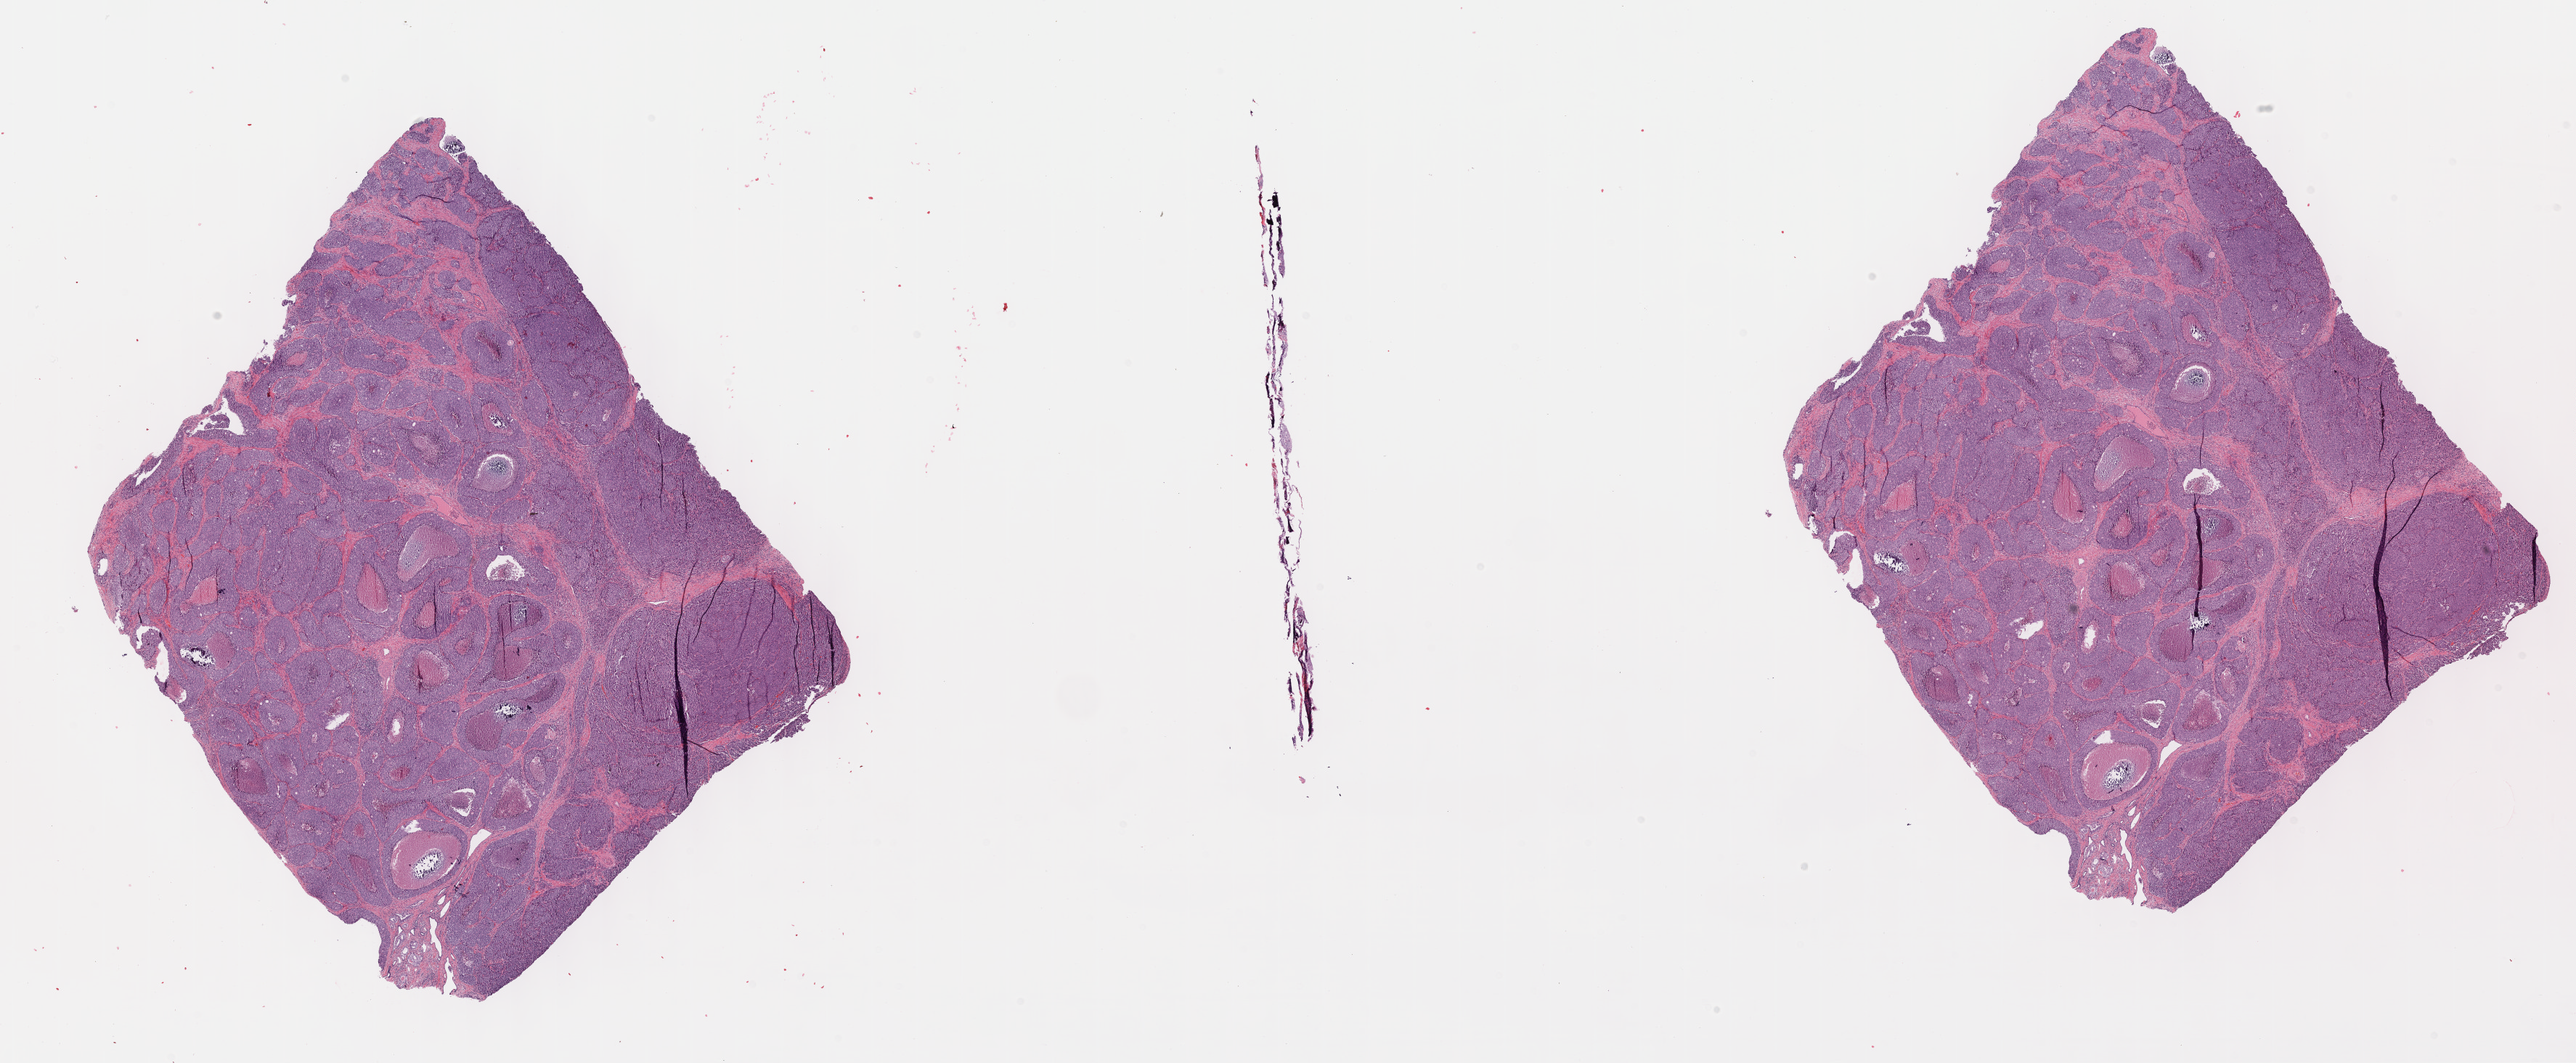
Whole-slide histology image, H&E-stained, a low-resolution overview of the entire scanned area, about 28.7 x 11.8 mm, formalin-fixed paraffin-embedded (FFPE) diagnostic section, primary tumour sample from the prostate. Male, age 78 years at initial diagnosis. Gleason score: 9 (5+4).
Pathologic diagnosis: Adenocarcinoma, NOS (prostate gland).